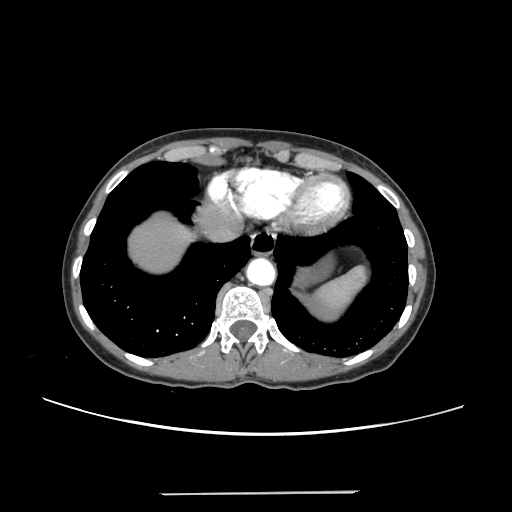
Contrast-enhanced abdominal CT, one axial slice. Position 222 of 240 along the scan axis. 120 kVp. Intravenous contrast given. Soft-tissue window (W 400 / L 40 HU). 1.25 mm slice thickness. 512 × 512 image matrix, field of view 371 × 371 mm. Female patient, age 60 years. From the clinical record (not read from this slice): diagnosis: colorectal cancer liver metastases, imaged before liver resection; multiple liver metastases: no; largest metastasis: 1.5 cm; disease in both lobes: no.
Annotated regions visible in this slice (expert manual segmentation):
- liver: bounding box [x1, y1, x2, y2] px = [130, 219, 190, 272]
- planned liver remnant (the part of the liver to remain after resection): [130, 216, 210, 272]